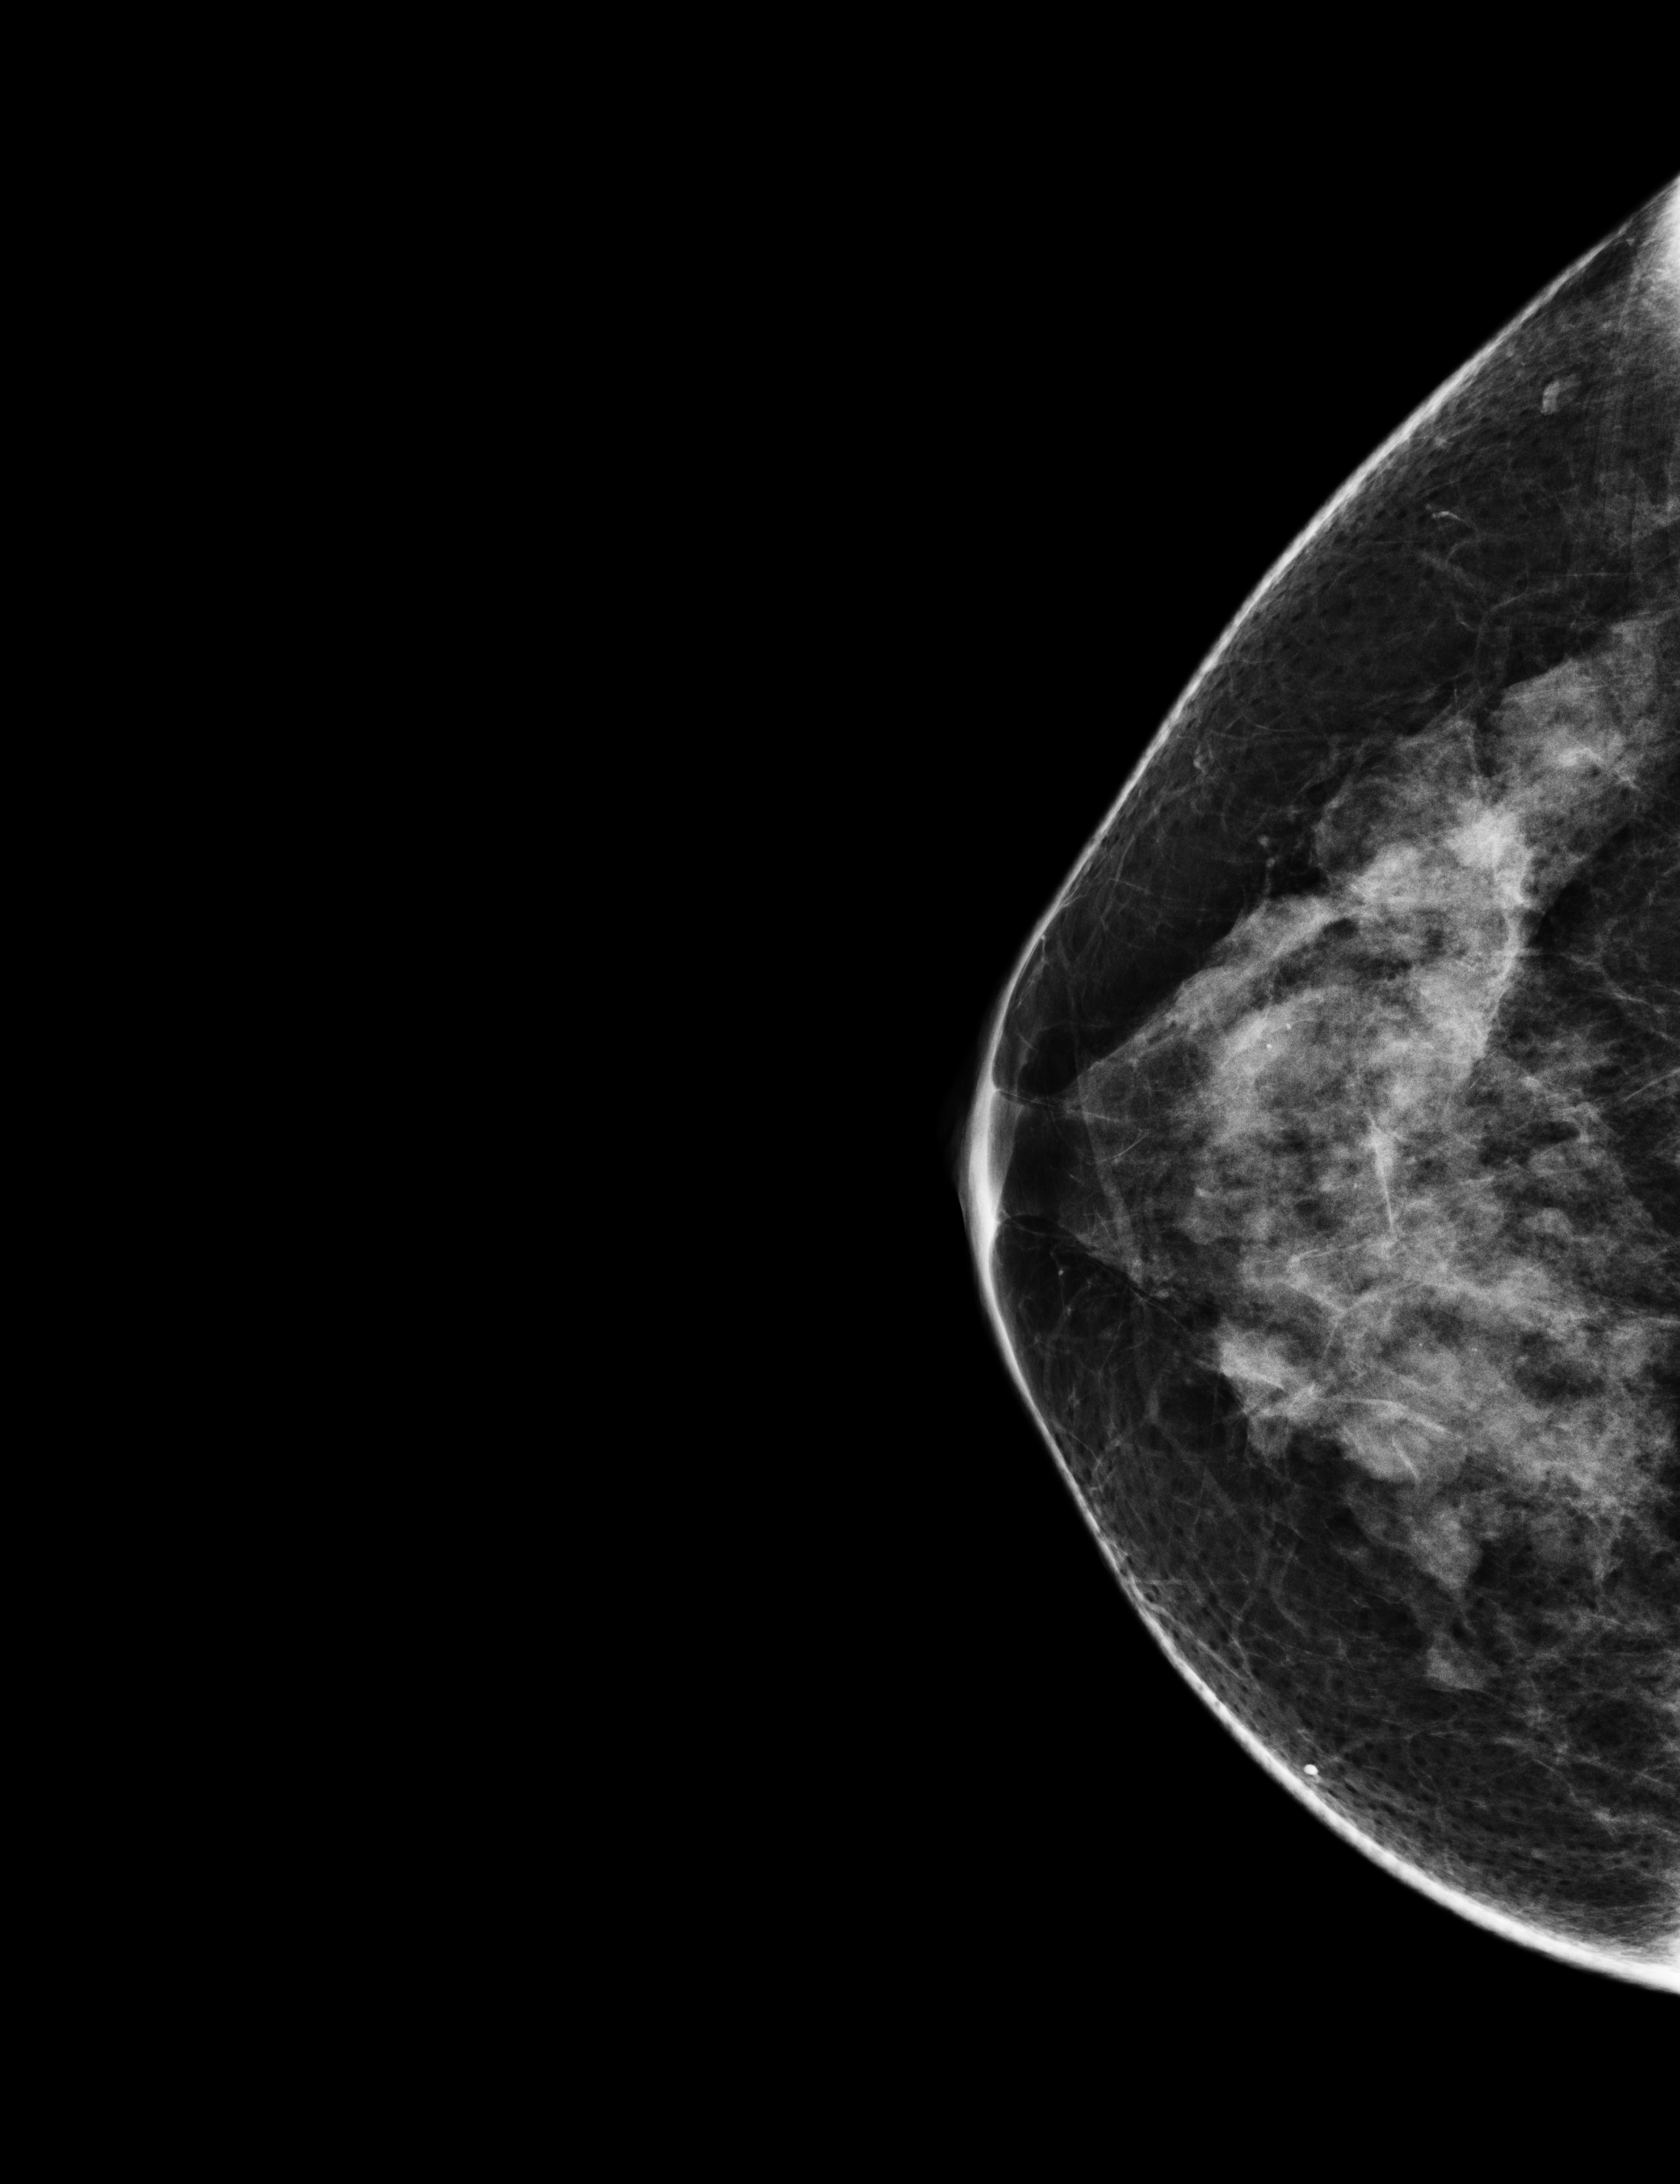
Full-field digital mammogram (FFDM); right breast; cranio-caudal projection; screening examination; compressed breast thickness 62 mm. Patient aged 58 years (female).
- breast density at the screening exam (both breasts): heterogeneously dense (BI-RADS density category c)
- final BI-RADS assessment for this screening round (tomosynthesis exam, both breasts): category 4
- recall: recalled for additional imaging after this screen